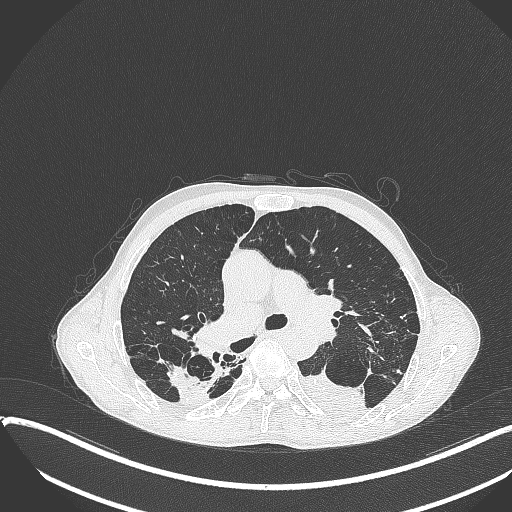
Chest CT, one axial slice; position 242 of 401 along the scan axis; reconstruction kernel B70f; lung window (W 1500 / L -600 HU); 1 mm slice thickness; 512 × 512 image matrix. Patient: male, 57 years. From the clinical record (not read from this slice): clinical TNM (as recorded): T4 N0 M0.
Structures marked on this image (bounding box drawn by a radiologist):
- lung tumour (recorded histology: squamous cell carcinoma): bounding box [x1, y1, x2, y2] px = [301, 368, 369, 418]